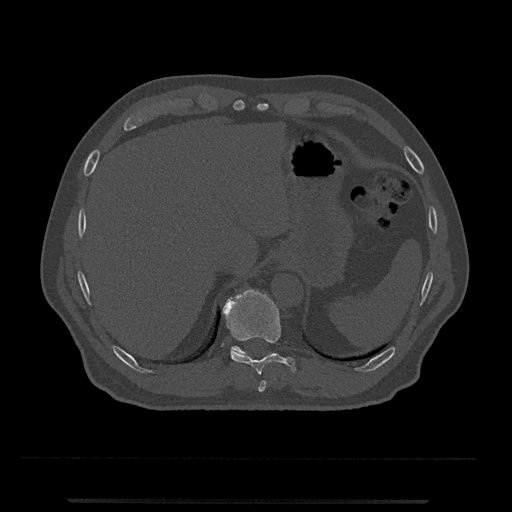
CT including the spine, one axial slice. Slice 509 of 797 in the series (ordered by position). Reconstruction kernel Br40s/3. 120 kVp. Bone window (W 1800 / L 400 HU). 0.5 mm slice thickness. 512 × 512 image matrix, field of view 419 × 419 mm. Male patient, age 63 years. Case-level facts recorded for this patient, not image findings: primary cancer: prostate.
Annotated regions visible in this slice (semi-automatic segmentation, software-assisted and operator-edited):
- T10 vertebra: bounding box (x1, y1, x2, y2) in pixels: (222, 289, 296, 375)
- T11 vertebra: (231, 346, 273, 356)
- T9 vertebra: (258, 380, 267, 392)